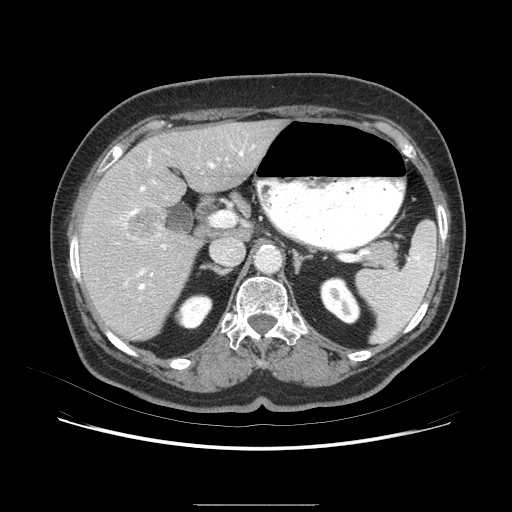
Contrast-enhanced abdominal CT (liver protocol), one axial slice. Slice 44 of 79 in the series (ordered by position). 120 kVp. Soft-tissue window (W 400 / L 40 HU). 2.5 mm slice thickness. 512 × 512 image matrix, field of view 380 × 380 mm. Case-level facts recorded for this patient, not image findings: diagnosis: hepatocellular carcinoma (patient treated with transarterial chemoembolisation; whether this scan precedes or follows treatment is not stated here); TNM stage (as recorded): Stage-I; Child-Pugh class: A; tumour nodularity: uninodular.
Structures marked on this image (semi-automatic segmentation, software-assisted and operator-edited):
- liver parenchyma outside the tumour (the mass and vessels are separate outlines, so this box may not span the whole liver): bounding box [x1, y1, x2, y2] px = [78, 122, 292, 344]
- mass: [125, 201, 169, 243]
- liver vessels: [86, 143, 268, 319]